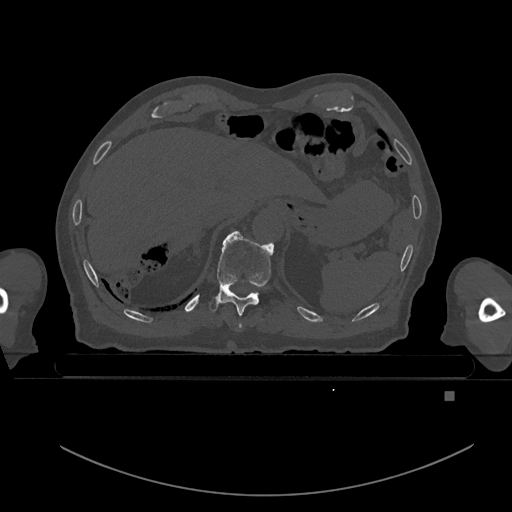
CT including the spine, one axial slice. Position 84 of 969 along the scan axis. Bone window (W 1800 / L 400 HU). 512 × 512 image matrix, field of view 456 × 456 mm. Patient: male, 82 years. Case-level facts recorded for this patient, not image findings: primary cancer: prostate; vertebrae with lytic lesions (as recorded): T11, T9, T8, T2.
Outlined on this slice (semi-automatic segmentation, software-assisted and operator-edited):
- T10 vertebra: bounding box (x1, y1, x2, y2) in pixels: (208, 231, 274, 315)